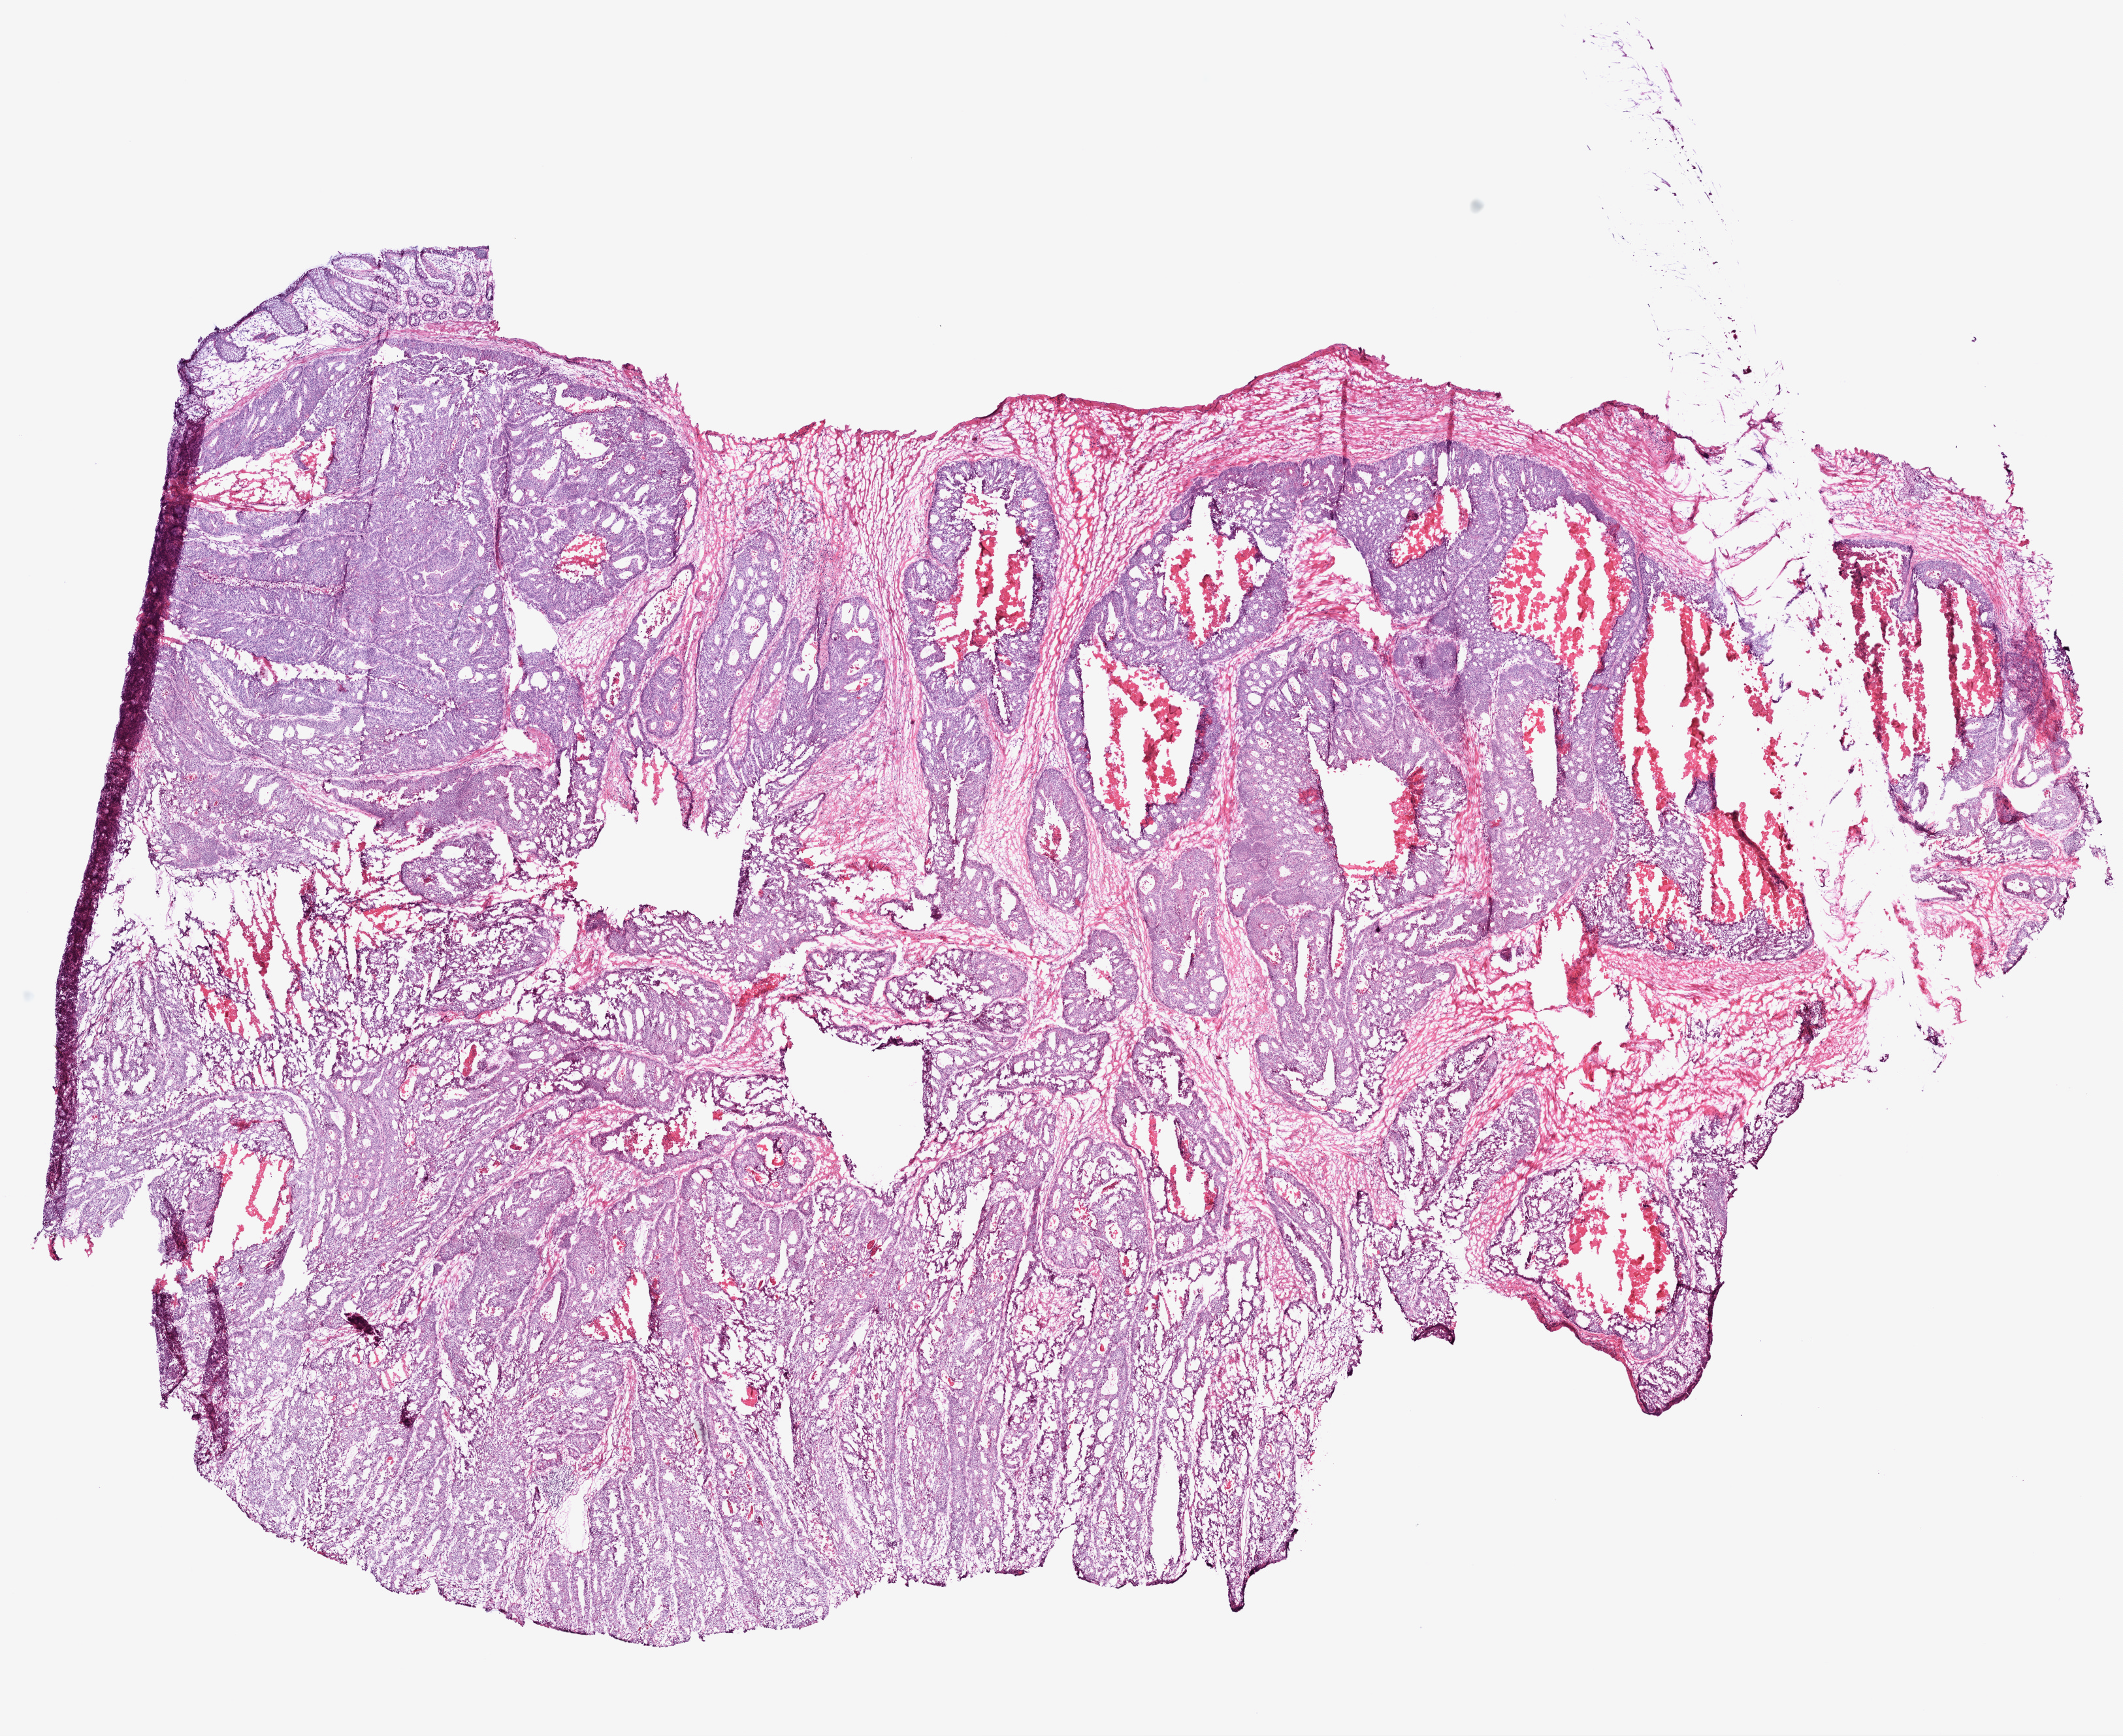
Whole-slide histology image, H&E-stained, low-resolution overview of the scanned area, about 13.0 x 10.7 mm (from a 20x scan). Frozen section from the top of the tissue portion. Primary tumour sample from the rectum. Patient sex: female. Slide review estimates, as recorded: tumour cells 68%, tumour nuclei 75%, normal cells 2%, stromal cells 10%, necrosis 20%.
AJCC pathologic stage: II (5th edition). Histologic diagnosis: Adenocarcinoma, NOS. TNM: T3 N0 M0.